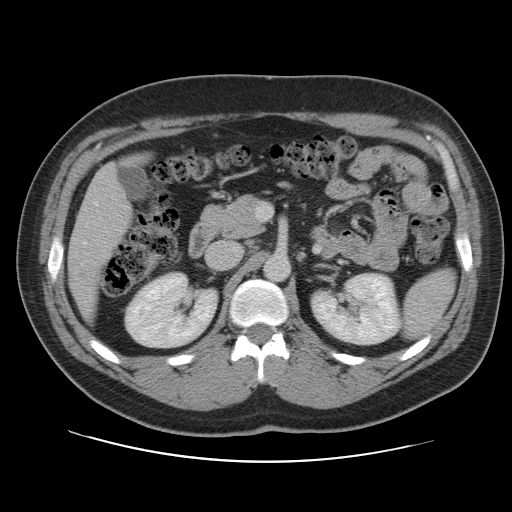
Contrast-enhanced abdominal CT, one axial slice. Position 56 of 109 along the scan axis. 120 kVp. Intravenous contrast given. Soft-tissue window (W 400 / L 40 HU). 5 mm slice thickness. 512 × 512 image matrix, field of view 402 × 402 mm. Male patient, age 35 years. Case-level facts recorded for this patient, not image findings: diagnosis: colorectal cancer liver metastases, imaged before liver resection; multiple liver metastases: yes.
Outlined on this slice (manually delineated by an expert):
- liver: box from (x=69, y=166) to (x=132, y=321) px
- planned liver remnant (the part of the liver to remain after resection): (x=69, y=166)–(x=132, y=321)